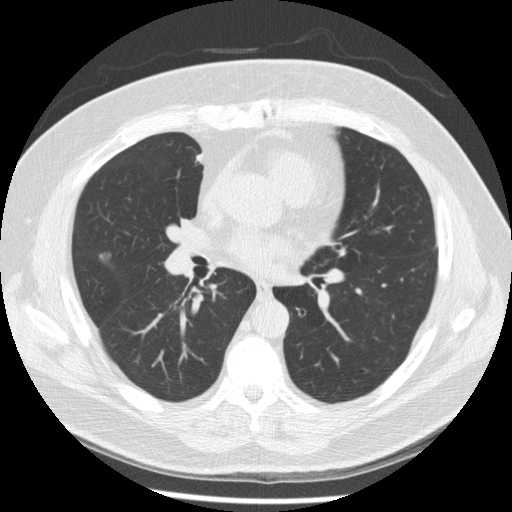
Low-dose screening chest CT, one axial slice; reconstruction kernel STANDARD; lung window (W 1500 / L -600 HU); 2.5 mm slice thickness; 512 × 512 image matrix, field of view 360 × 360 mm.
Structures marked on this image (outlined manually by an expert reader):
- lesion 1 (tumor, middle lobe of right lung): box from (x=99, y=250) to (x=115, y=265) px